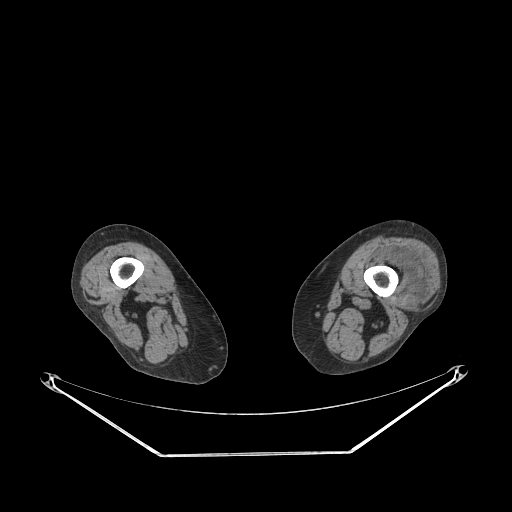
CT of an extremity soft-tissue mass (from a PET/CT study), one axial slice. Slice 196 of 267 in the series (ordered by position). Reconstruction kernel STANDARD. Soft-tissue window (W 400 / L 40 HU). 3.75 mm slice thickness. 512 × 512 image matrix, field of view 500 × 500 mm. Female patient. Case-level facts recorded for this patient, not image findings: histological type: undifferentiated – high grade; grade: high; site of the primary tumour: left thigh.
Annotated regions visible in this slice (expert contour drawn on MRI and transferred to this co-registered scan by the dataset authors):
- gross tumour volume including surrounding oedema: box from (x=374, y=247) to (x=430, y=296) px